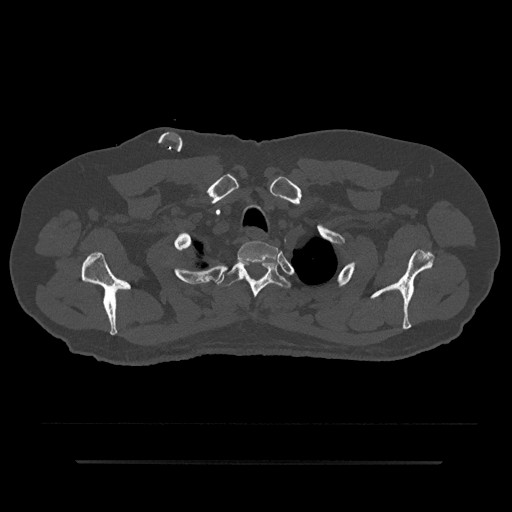
CT including the spine, one axial slice; slice 710 of 797 in the series (ordered by position); bone window (W 1800 / L 400 HU); 512 × 512 image matrix, field of view 464 × 464 mm. Male patient, age 59 years. Case-level facts recorded for this patient, not image findings: primary cancer: bile ducts; vertebrae with lytic lesions (as recorded): T10.
Annotated regions visible in this slice (semi-automatic segmentation, software-assisted and operator-edited):
- T1 vertebra: box from (x=237, y=241) to (x=278, y=264) px
- T2 vertebra: (x=216, y=262)–(x=291, y=298)